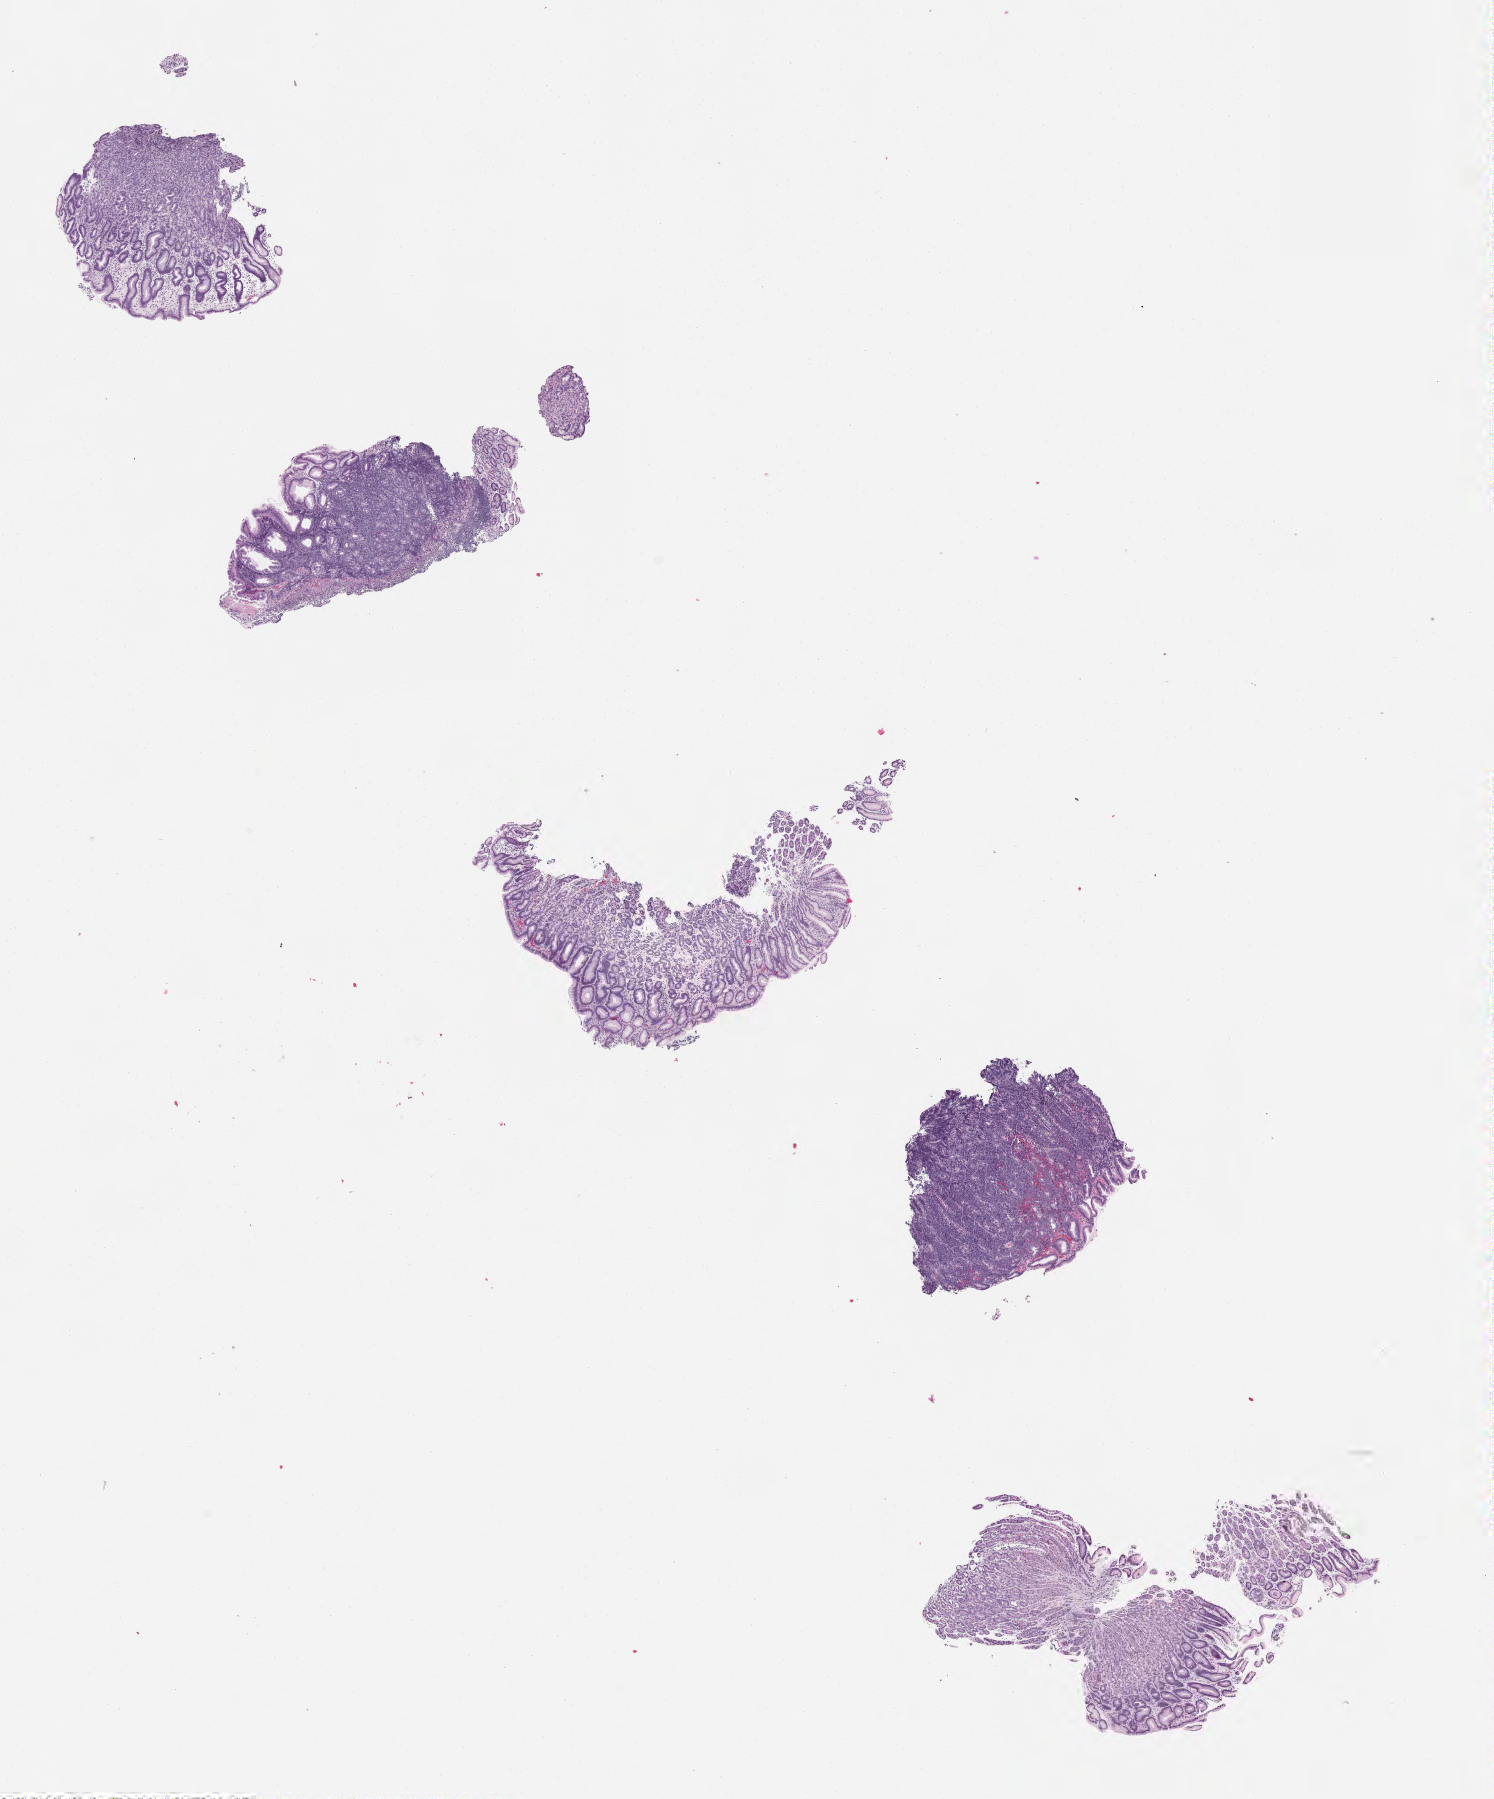
Whole-slide image, H&E stain — whole scanned area (about 12.0 x 14.5 mm) shown as a low-resolution overview. Tumor tissue. Patient male; aged 40.
Histologic diagnosis: Burkitt lymphoma, NOS.